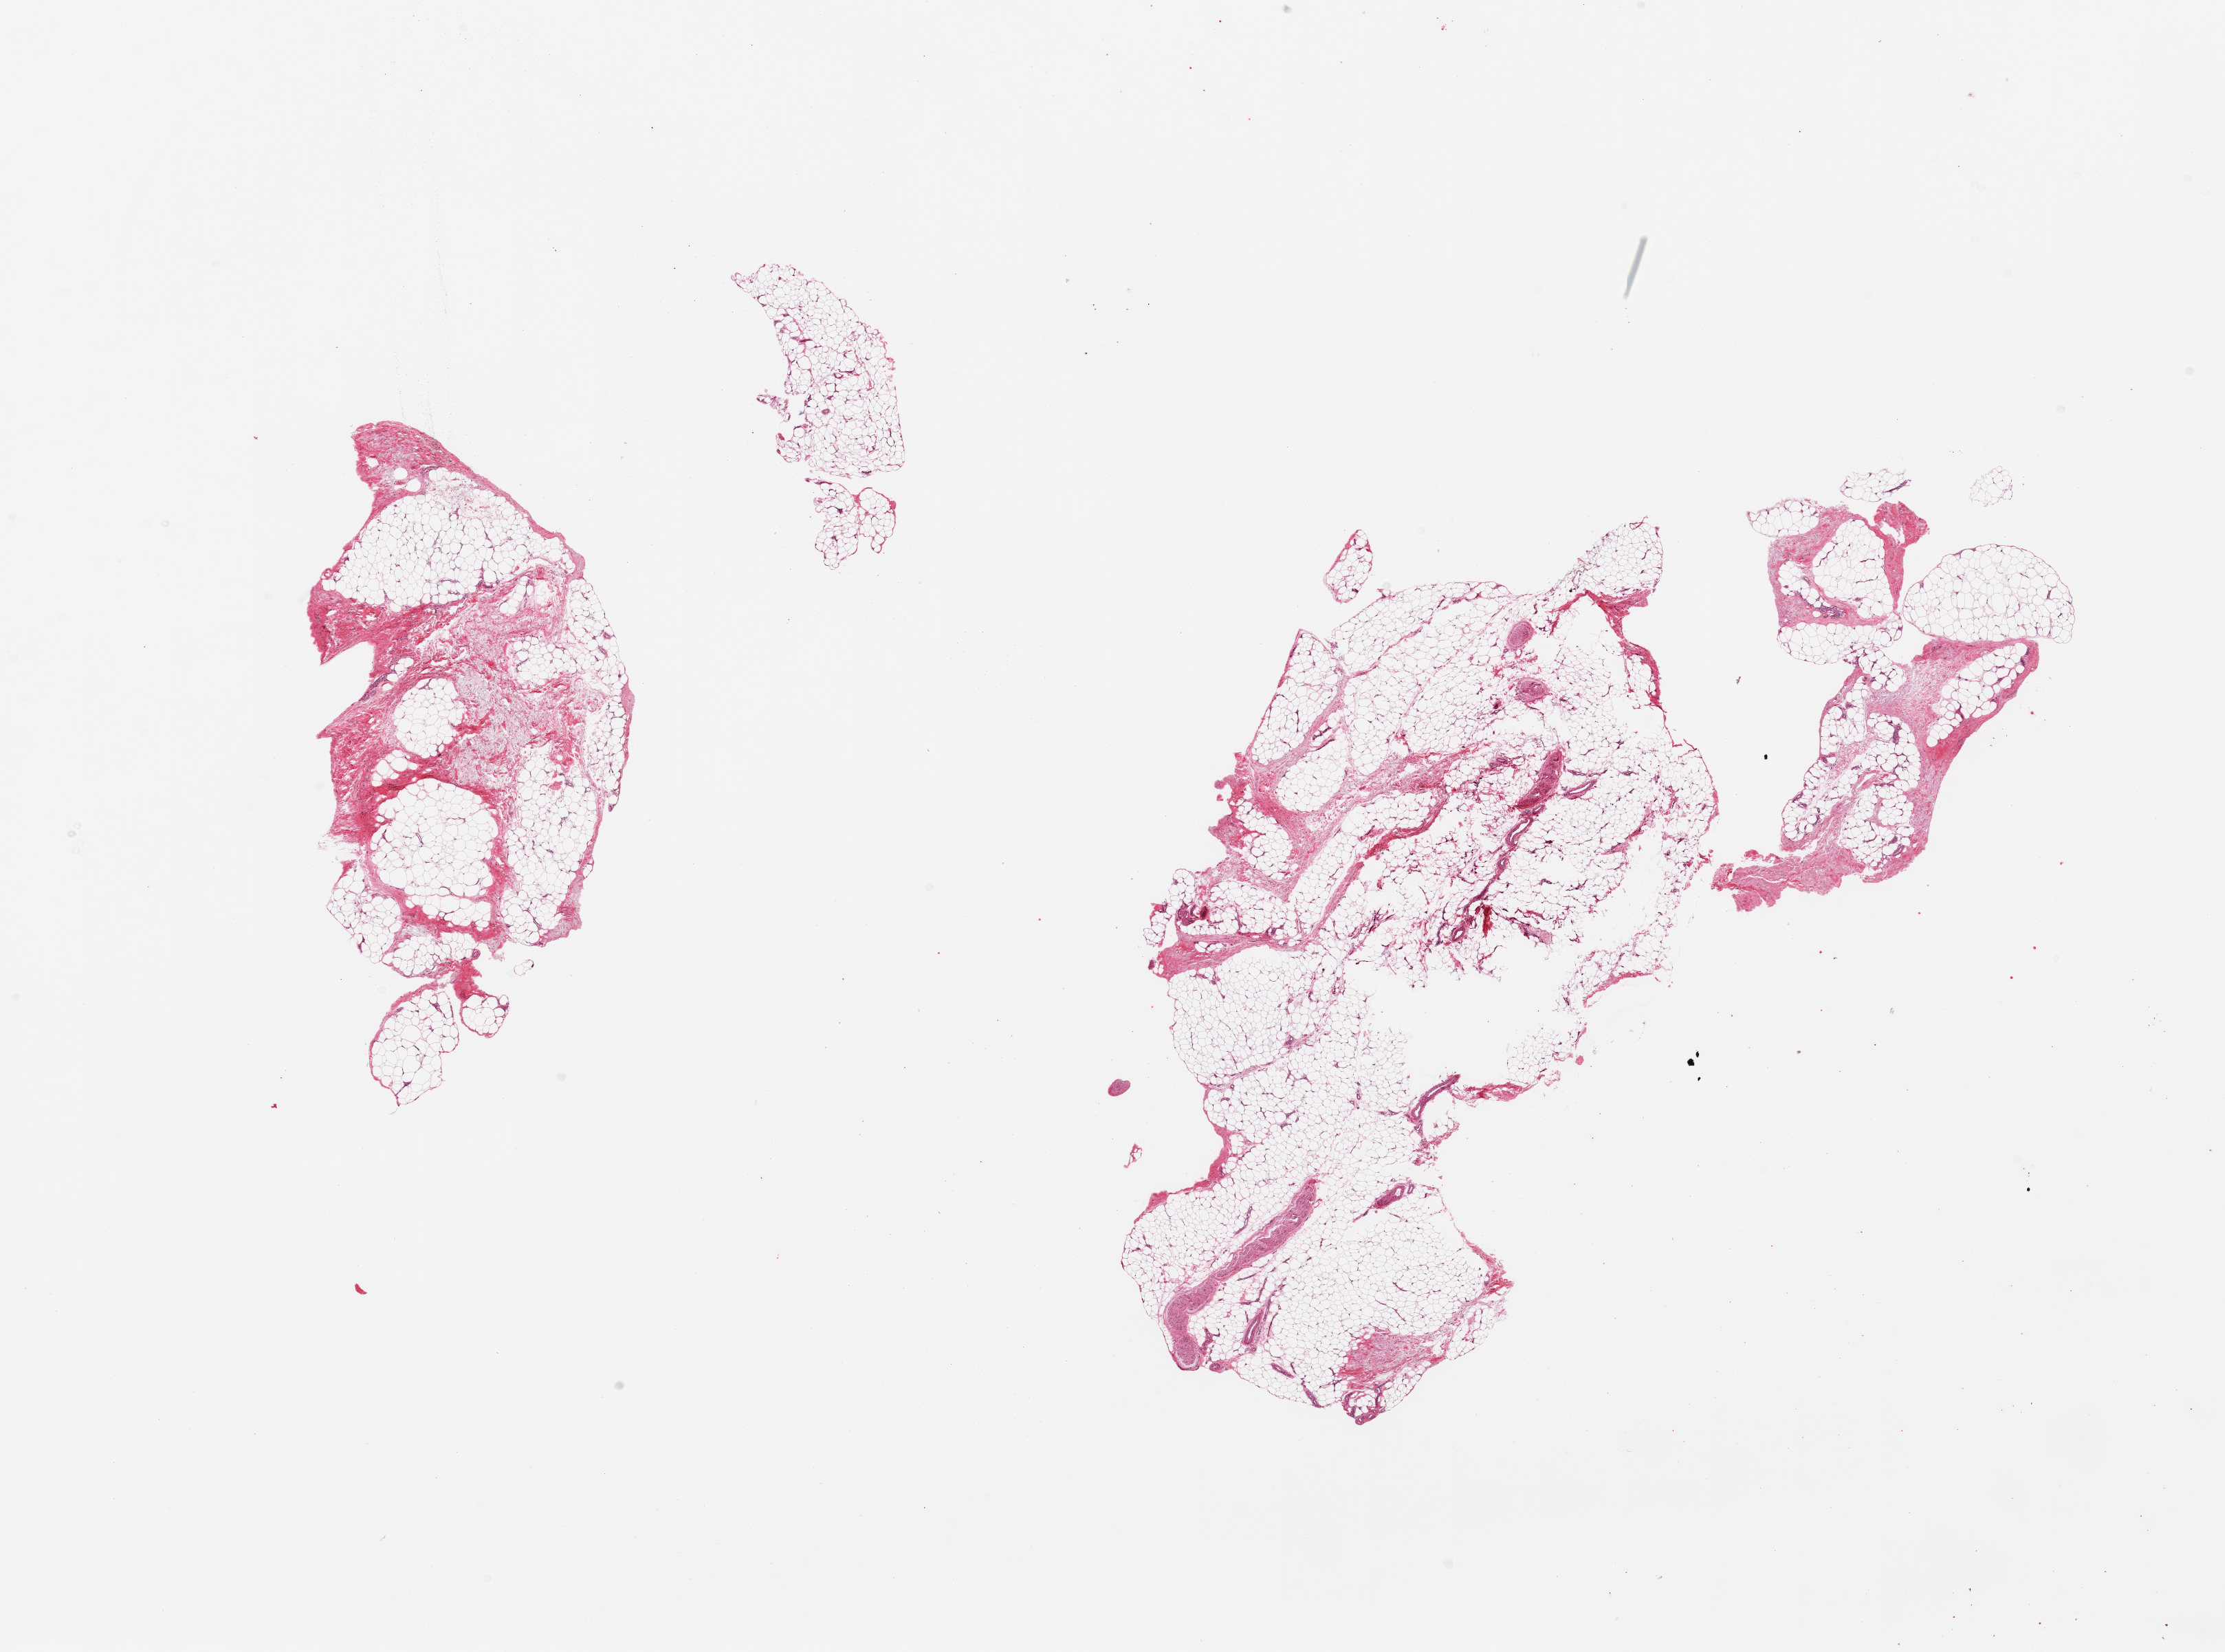
Whole-slide image, haematoxylin and eosin stain, whole scanned area (about 25.6 x 19.0 mm) shown as a low-resolution overview. PAXgene-fixed paraffin-embedded (PFPE) section. Target tissue: adipose tissue. Tissue donor sample. Donor: male.
* review note (as recorded): 2 pieces, ~15-20% fascia/vascular elements